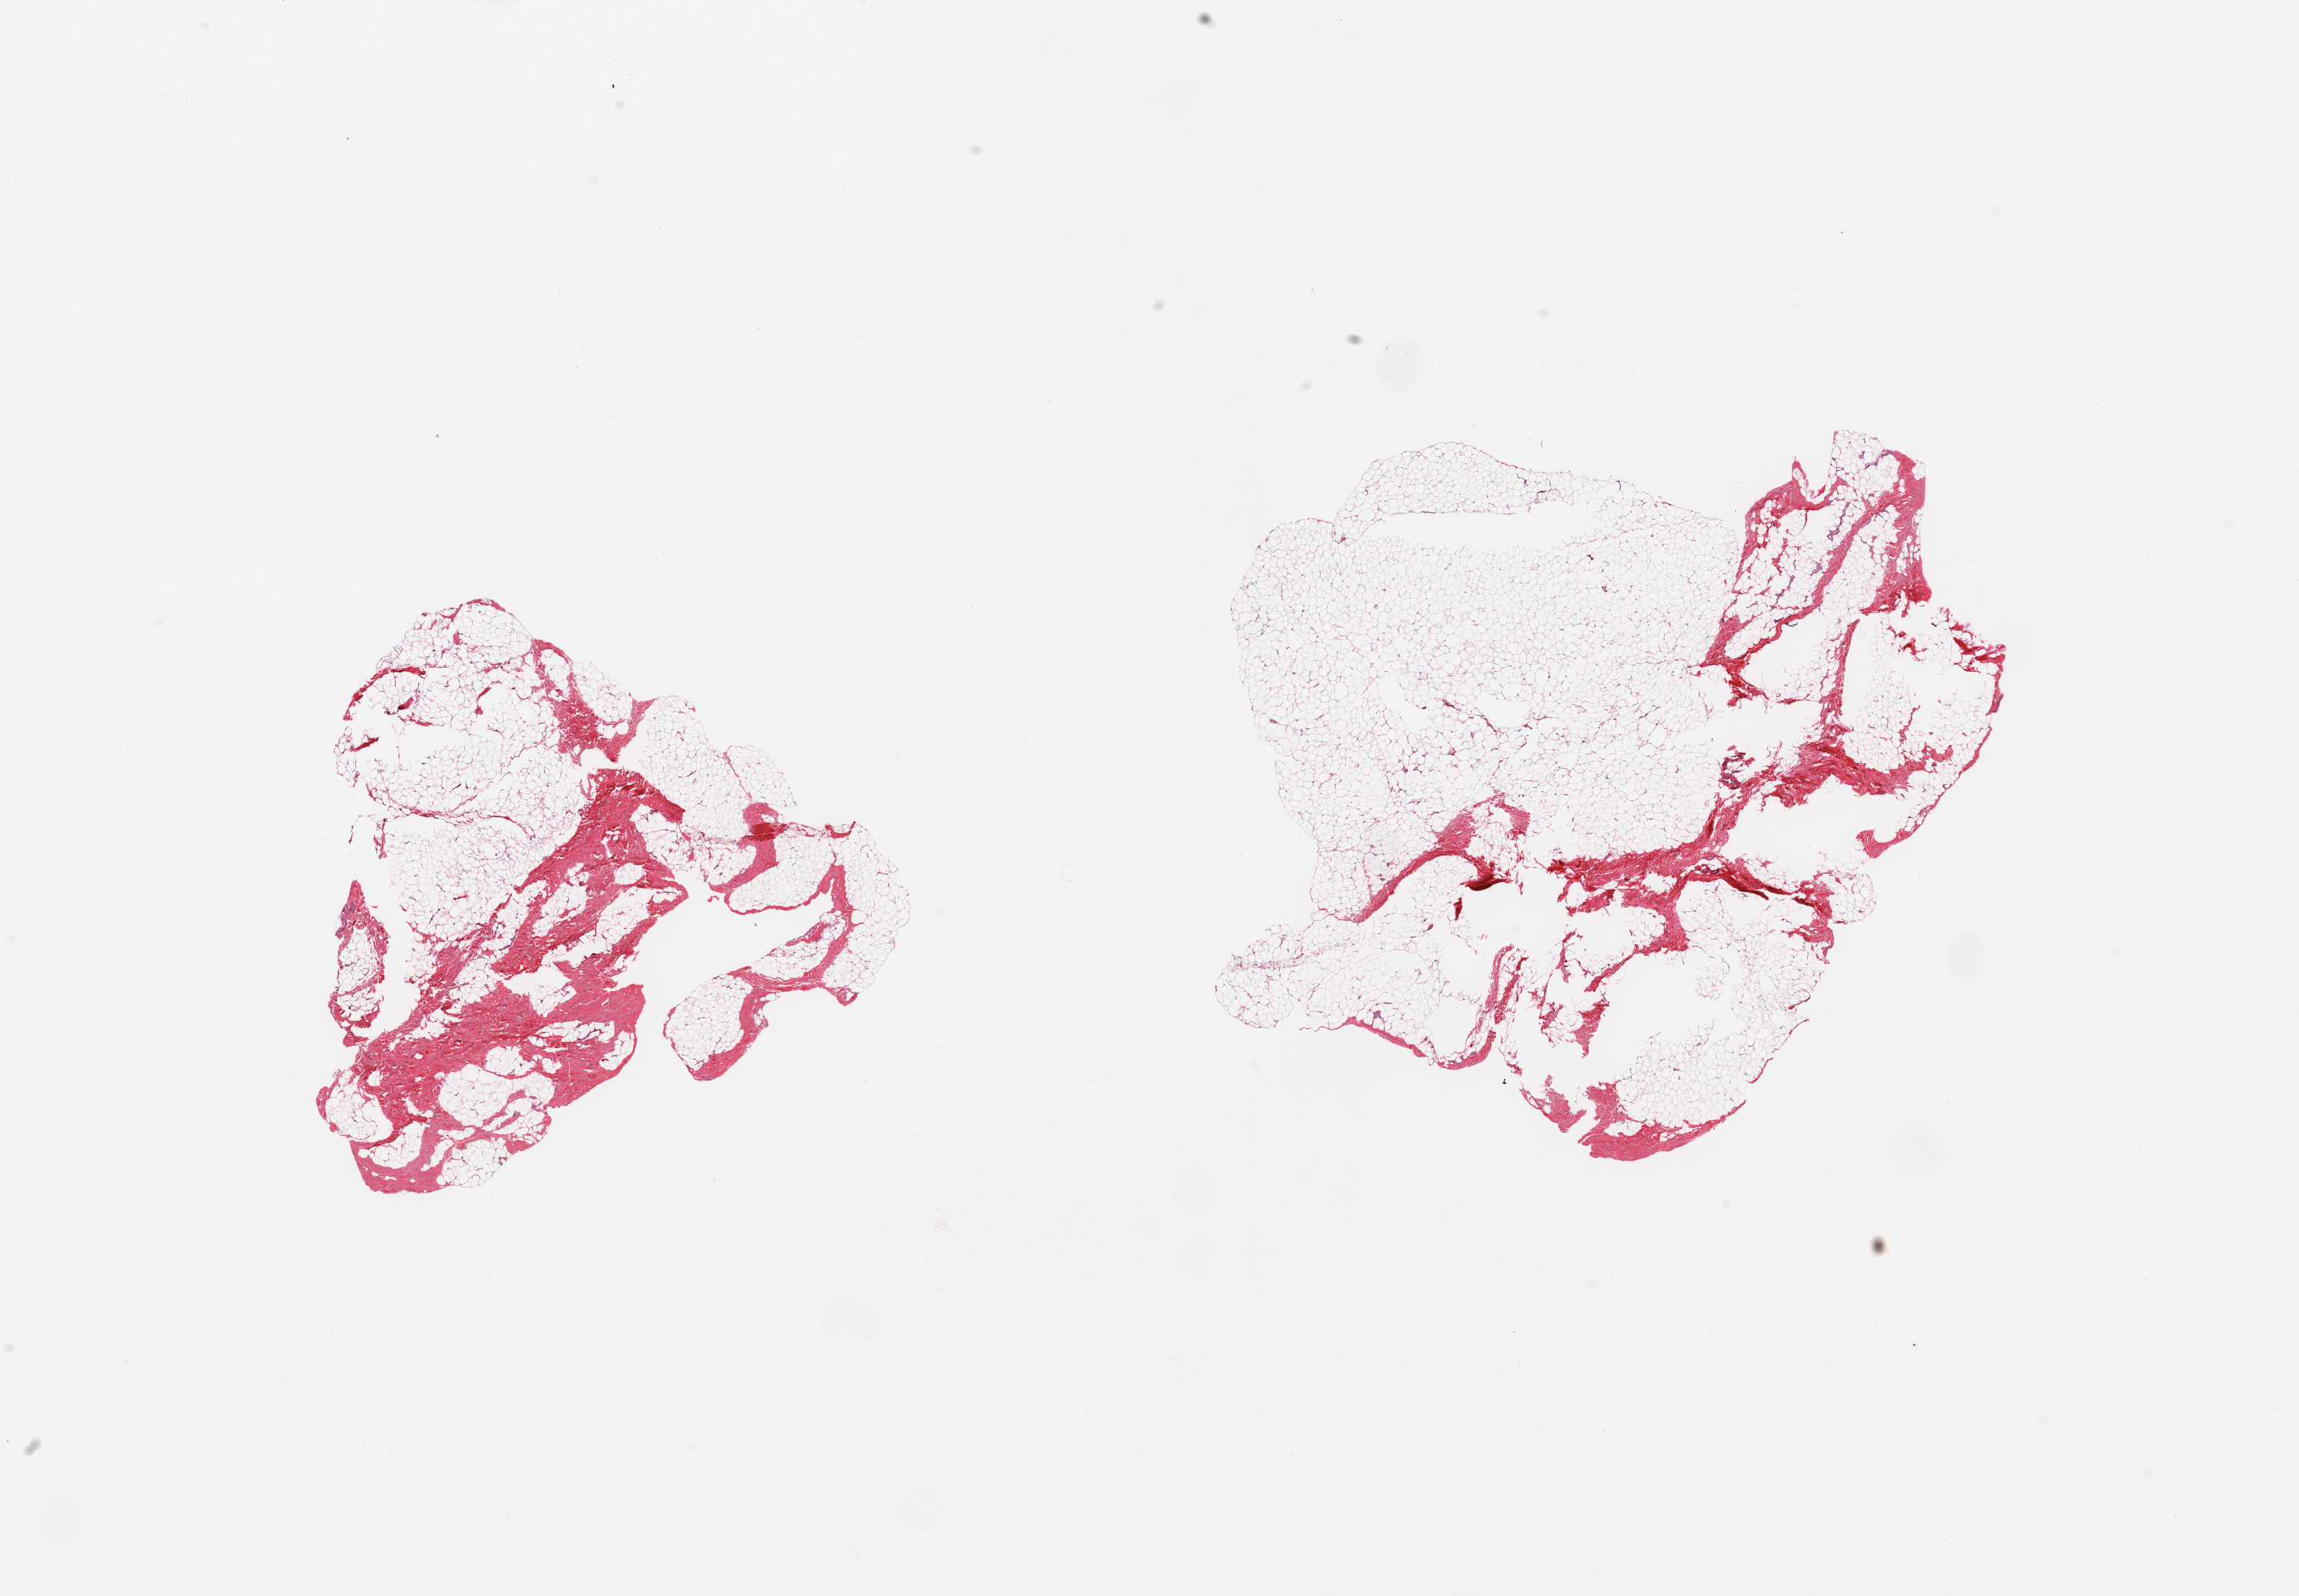
H&E whole-slide image — a low-resolution overview of the entire scanned area, about 23.6 x 16.4 mm (slide scanned at 20x); PAXgene-fixed paraffin-embedded (PFPE) section; target tissue: breast; tissue donor sample. Donor sex: male.
Reviewer comment on this tissue sample: 2 pieces; fat with ~15 and 30% fibrous tissue, no ductal elements seen.